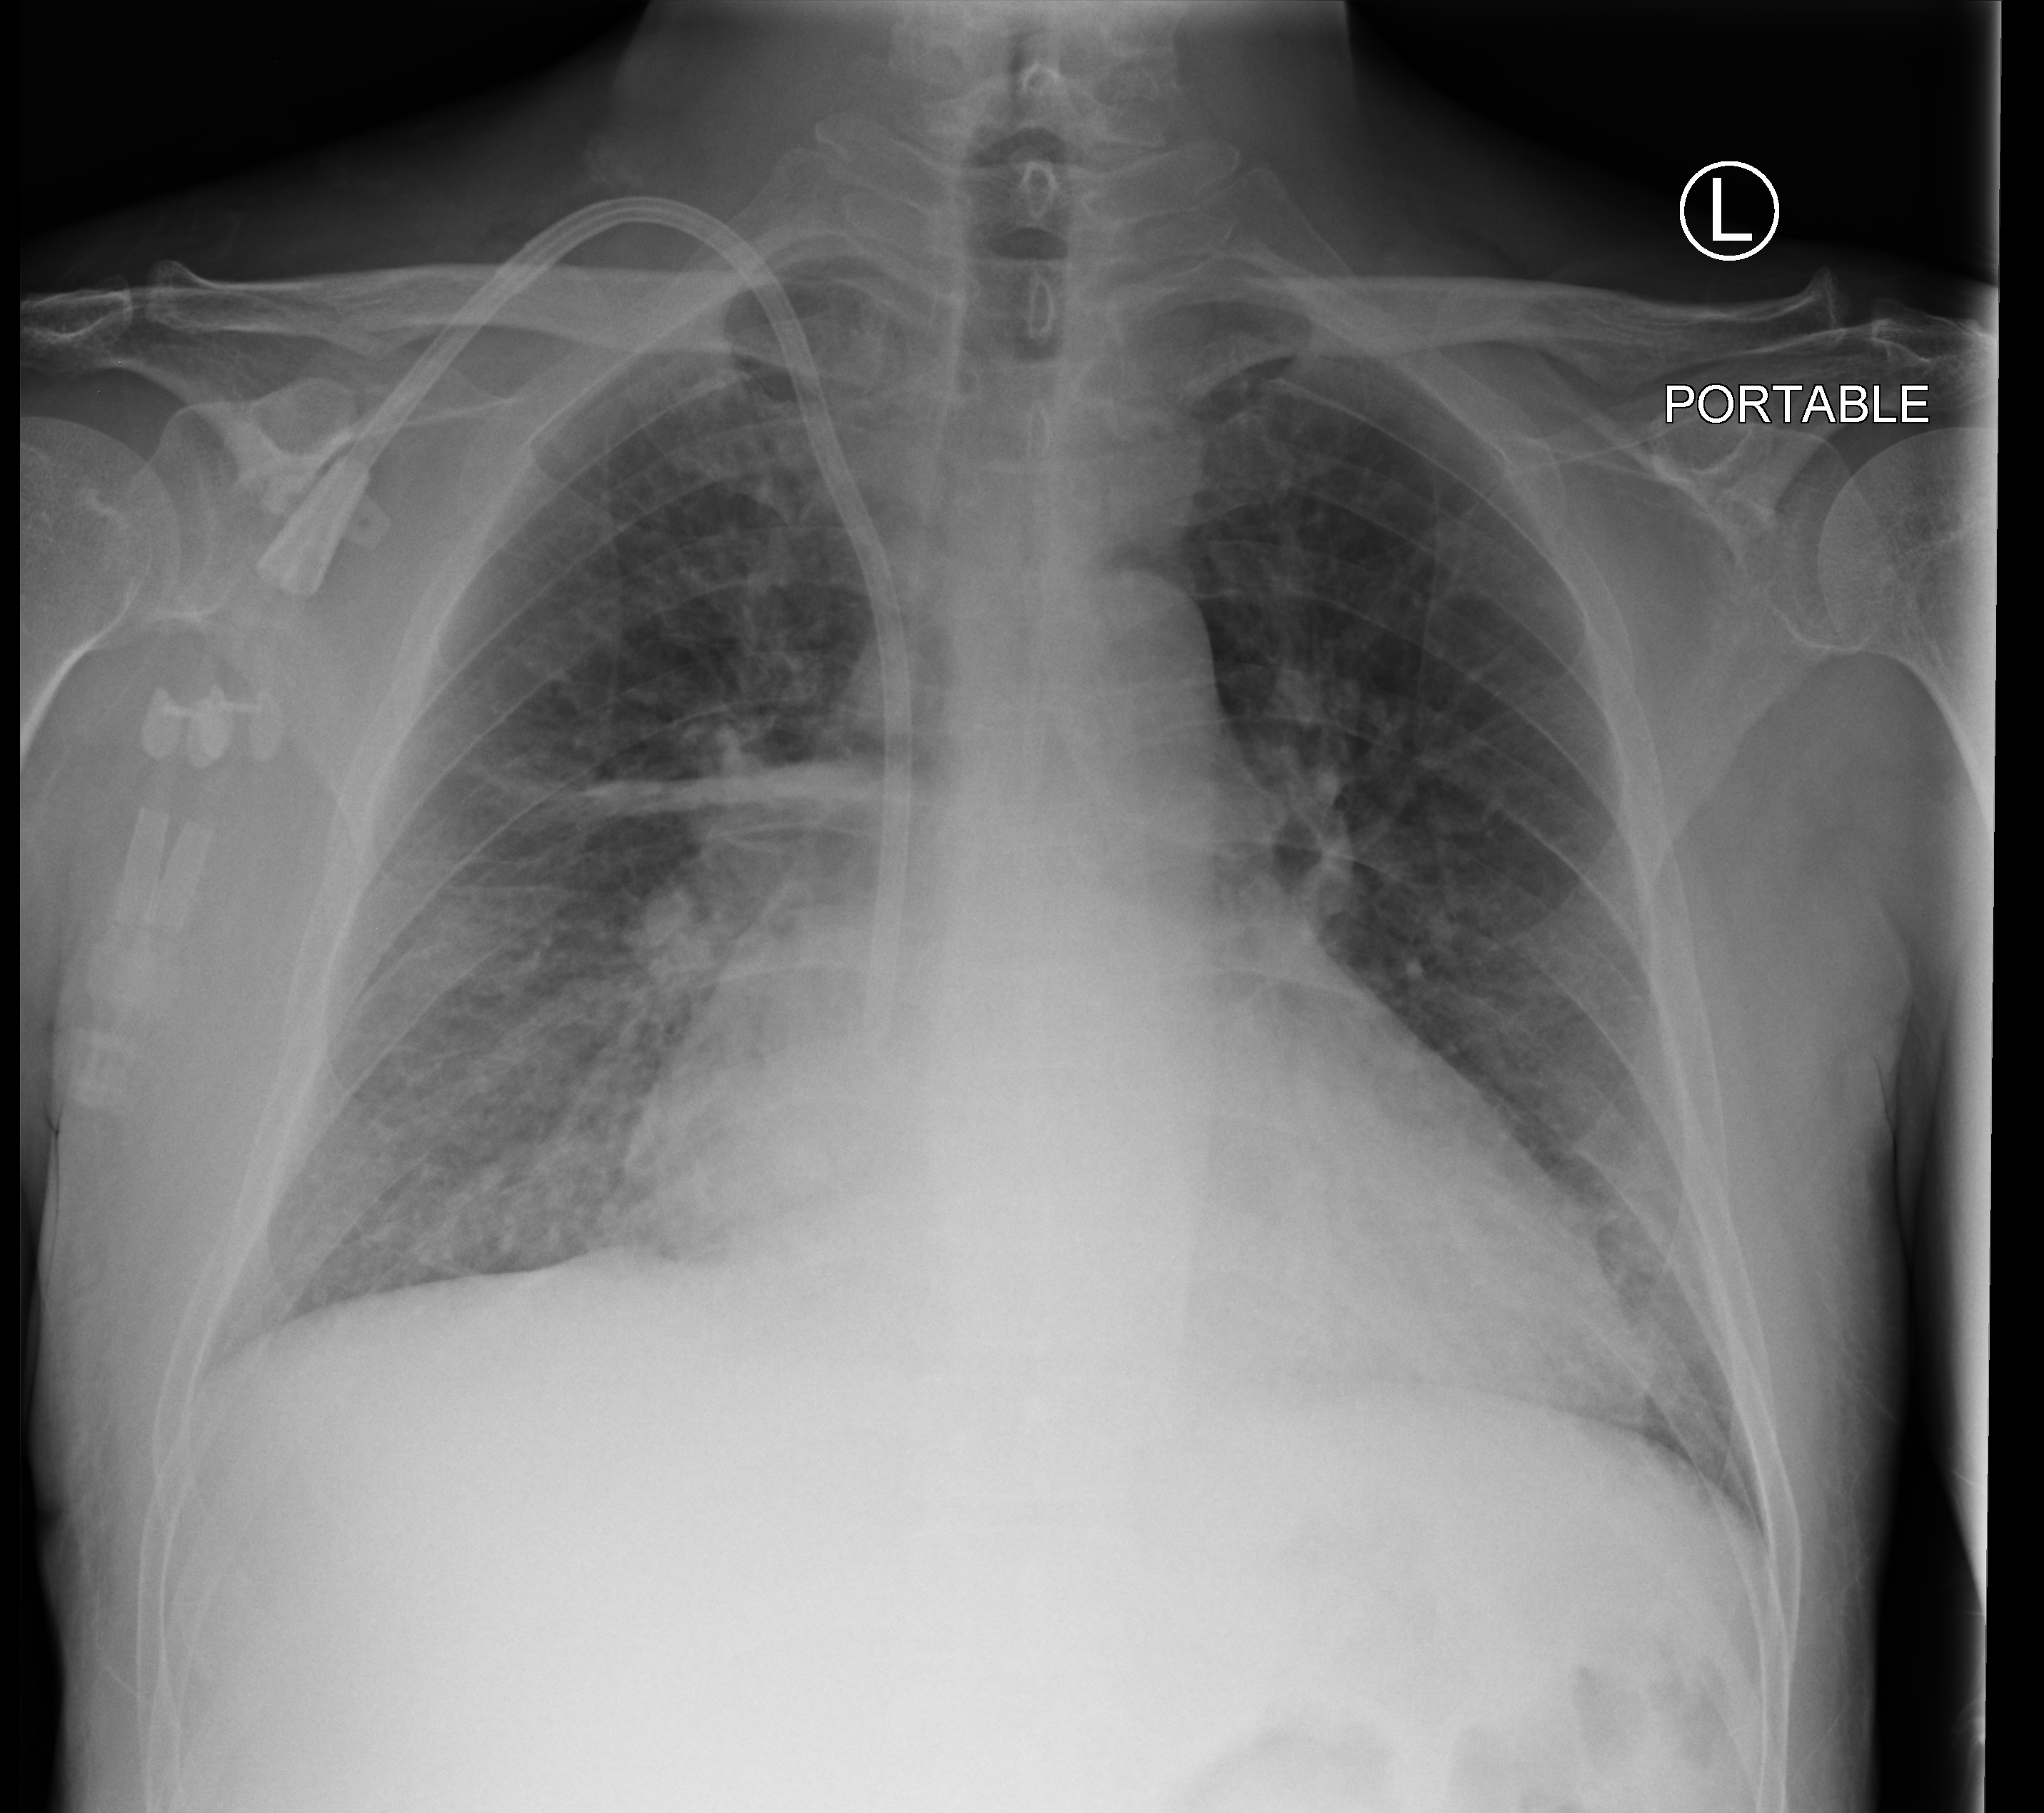
Portable chest radiograph; anteroposterior (AP) projection. Male patient hospitalised with COVID-19, age 18–59 years.
Hospital-stay facts (about this admission, not read from this image; timing relative to this image not recorded):
- mechanically ventilated during this hospital stay: no